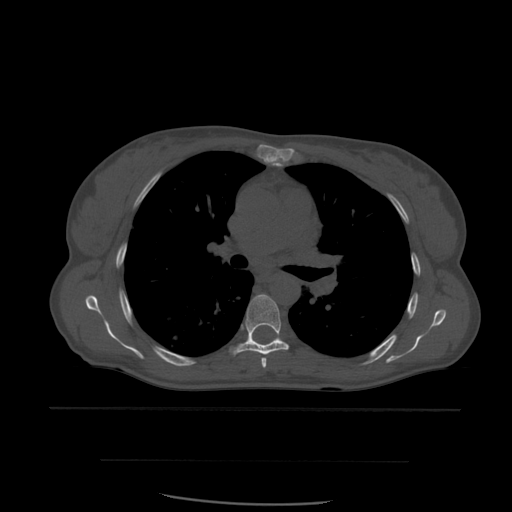
CT including the spine, one axial slice. Position 395 of 574 along the scan axis. Bone window (W 1800 / L 400 HU). 512 × 512 image matrix, field of view 392 × 392 mm. Patient age 48 years. From the clinical record (not read from this slice): primary cancer: lung; vertebrae with lytic lesions (as recorded): T11.
Outlined on this slice (semi-automatic segmentation, software-assisted and operator-edited):
- T5 vertebra: bounding box <261,357,267,368> (left, top, right, bottom; pixels)
- T6 vertebra: <231,294,289,355>